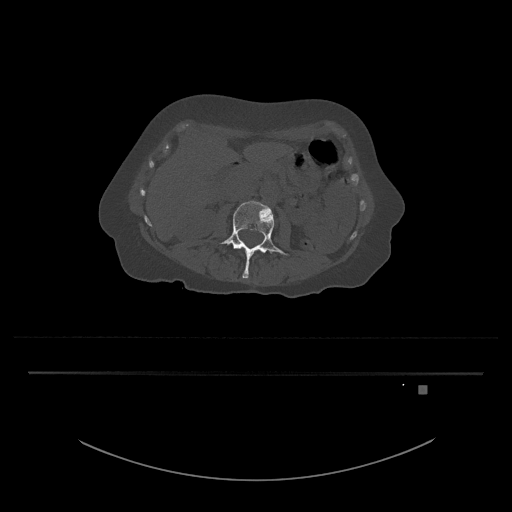
CT including the spine, one axial slice; position 431 of 797 along the scan axis; reconstruction kernel Br40s/3; 120 kVp; bone window (W 1800 / L 400 HU); 0.5 mm slice thickness; 512 × 512 image matrix, field of view 500 × 500 mm. Female patient, age 57 years. From the clinical record (not read from this slice): primary cancer: cervical.
Outlined on this slice (semi-automatic segmentation, software-assisted and operator-edited):
- L3 vertebra: box from (x=220, y=201) to (x=288, y=279) px